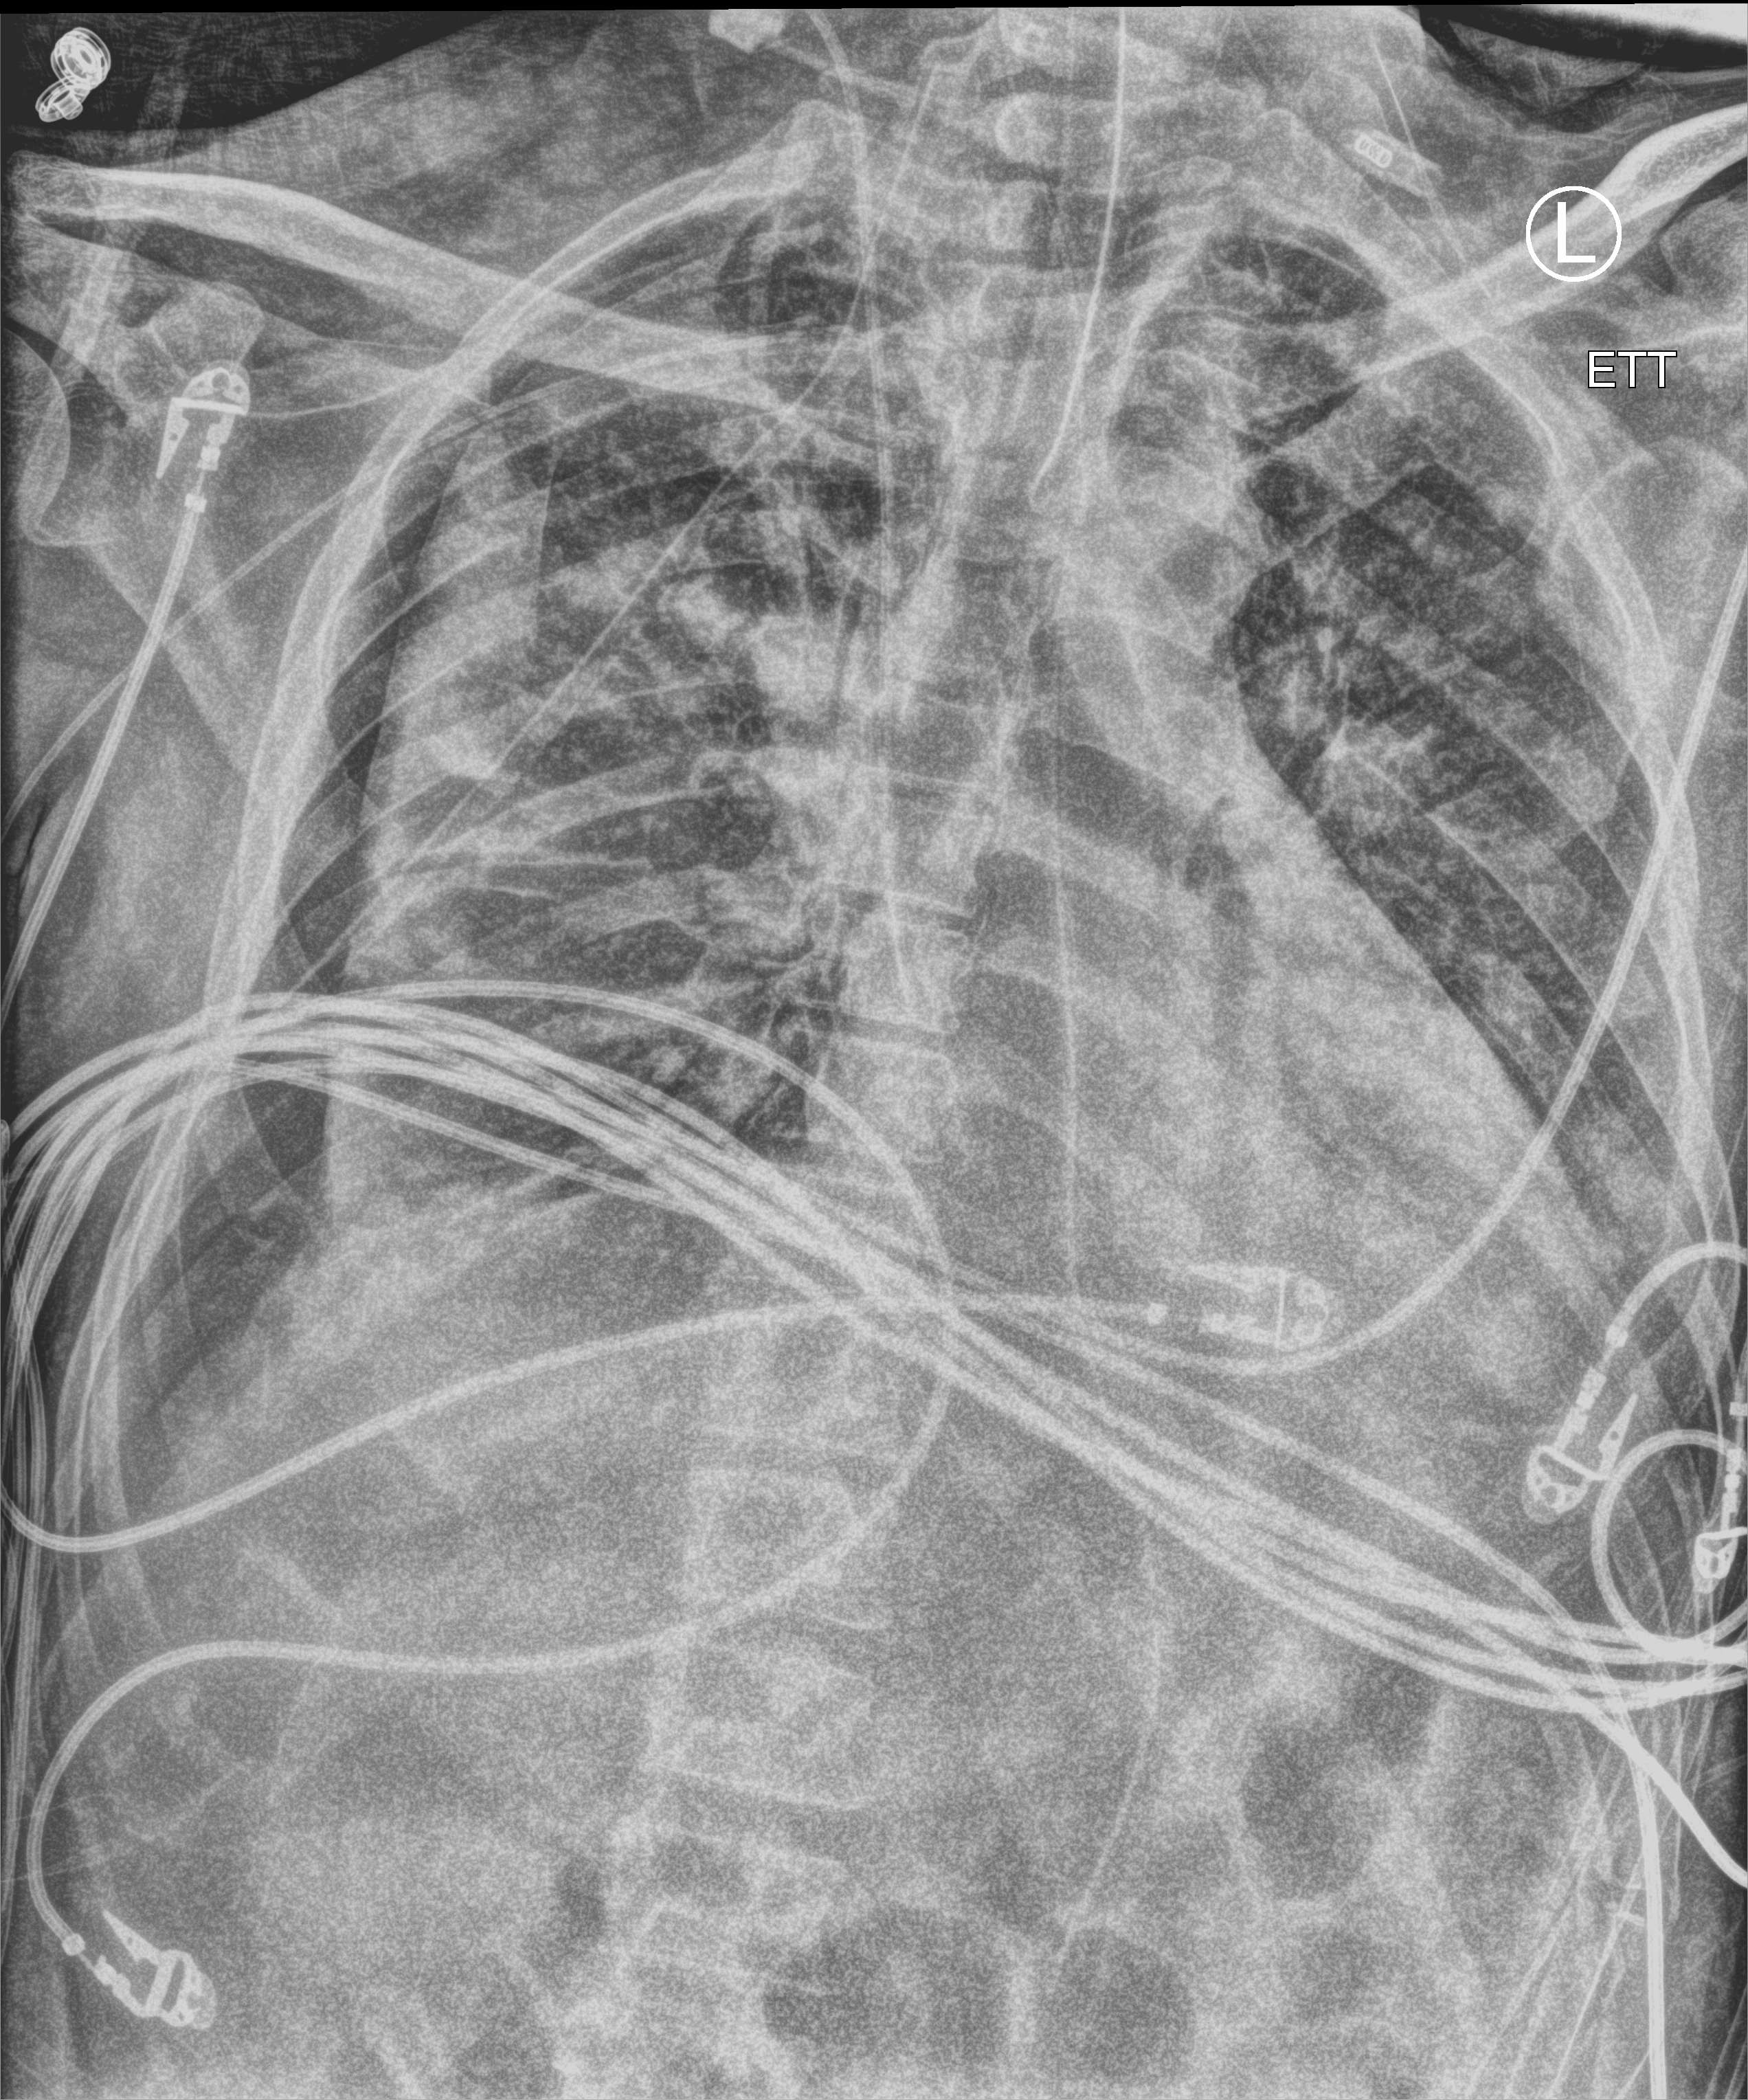
Bedside chest radiograph (computed radiography); anteroposterior (AP) projection. Patient hospitalised with COVID-19; male, aged 18–59 years.
Admission-level facts for this patient (not findings on this image; timing relative to this image not recorded):
- smoking status (admission record): never
- COPD (admission record): no
- mechanically ventilated during this hospital stay: yes